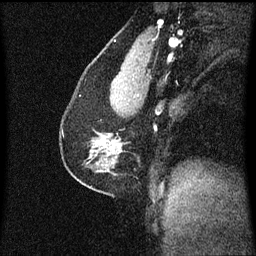
Breast MRI (dynamic contrast-enhanced), one sagittal slice. Position 35 of 60 along the scan axis. Dynamic contrast-enhanced series, image 2 of 3 at this slice position (ordered by acquisition). 1.5 T. TE 4.2 ms, TR 8.4 ms. 256 × 256 image matrix, field of view 200 × 200 mm. Female patient, age 41 years. From the clinical record (not read from this slice): setting: breast cancer imaged before/during neoadjuvant chemotherapy; receptor status: triple-negative.
Annotated regions visible in this slice (semi-automatically segmented with operator editing):
- analysis volume of interest (the breast-tissue region the enhancement analysis was run in; not a lesion): bounding box <61,104,125,175> (left, top, right, bottom; pixels)
- tumour enhancement mask (voxels above the 70 % enhancement threshold inside the analysis volume of interest): <111,142,115,145>